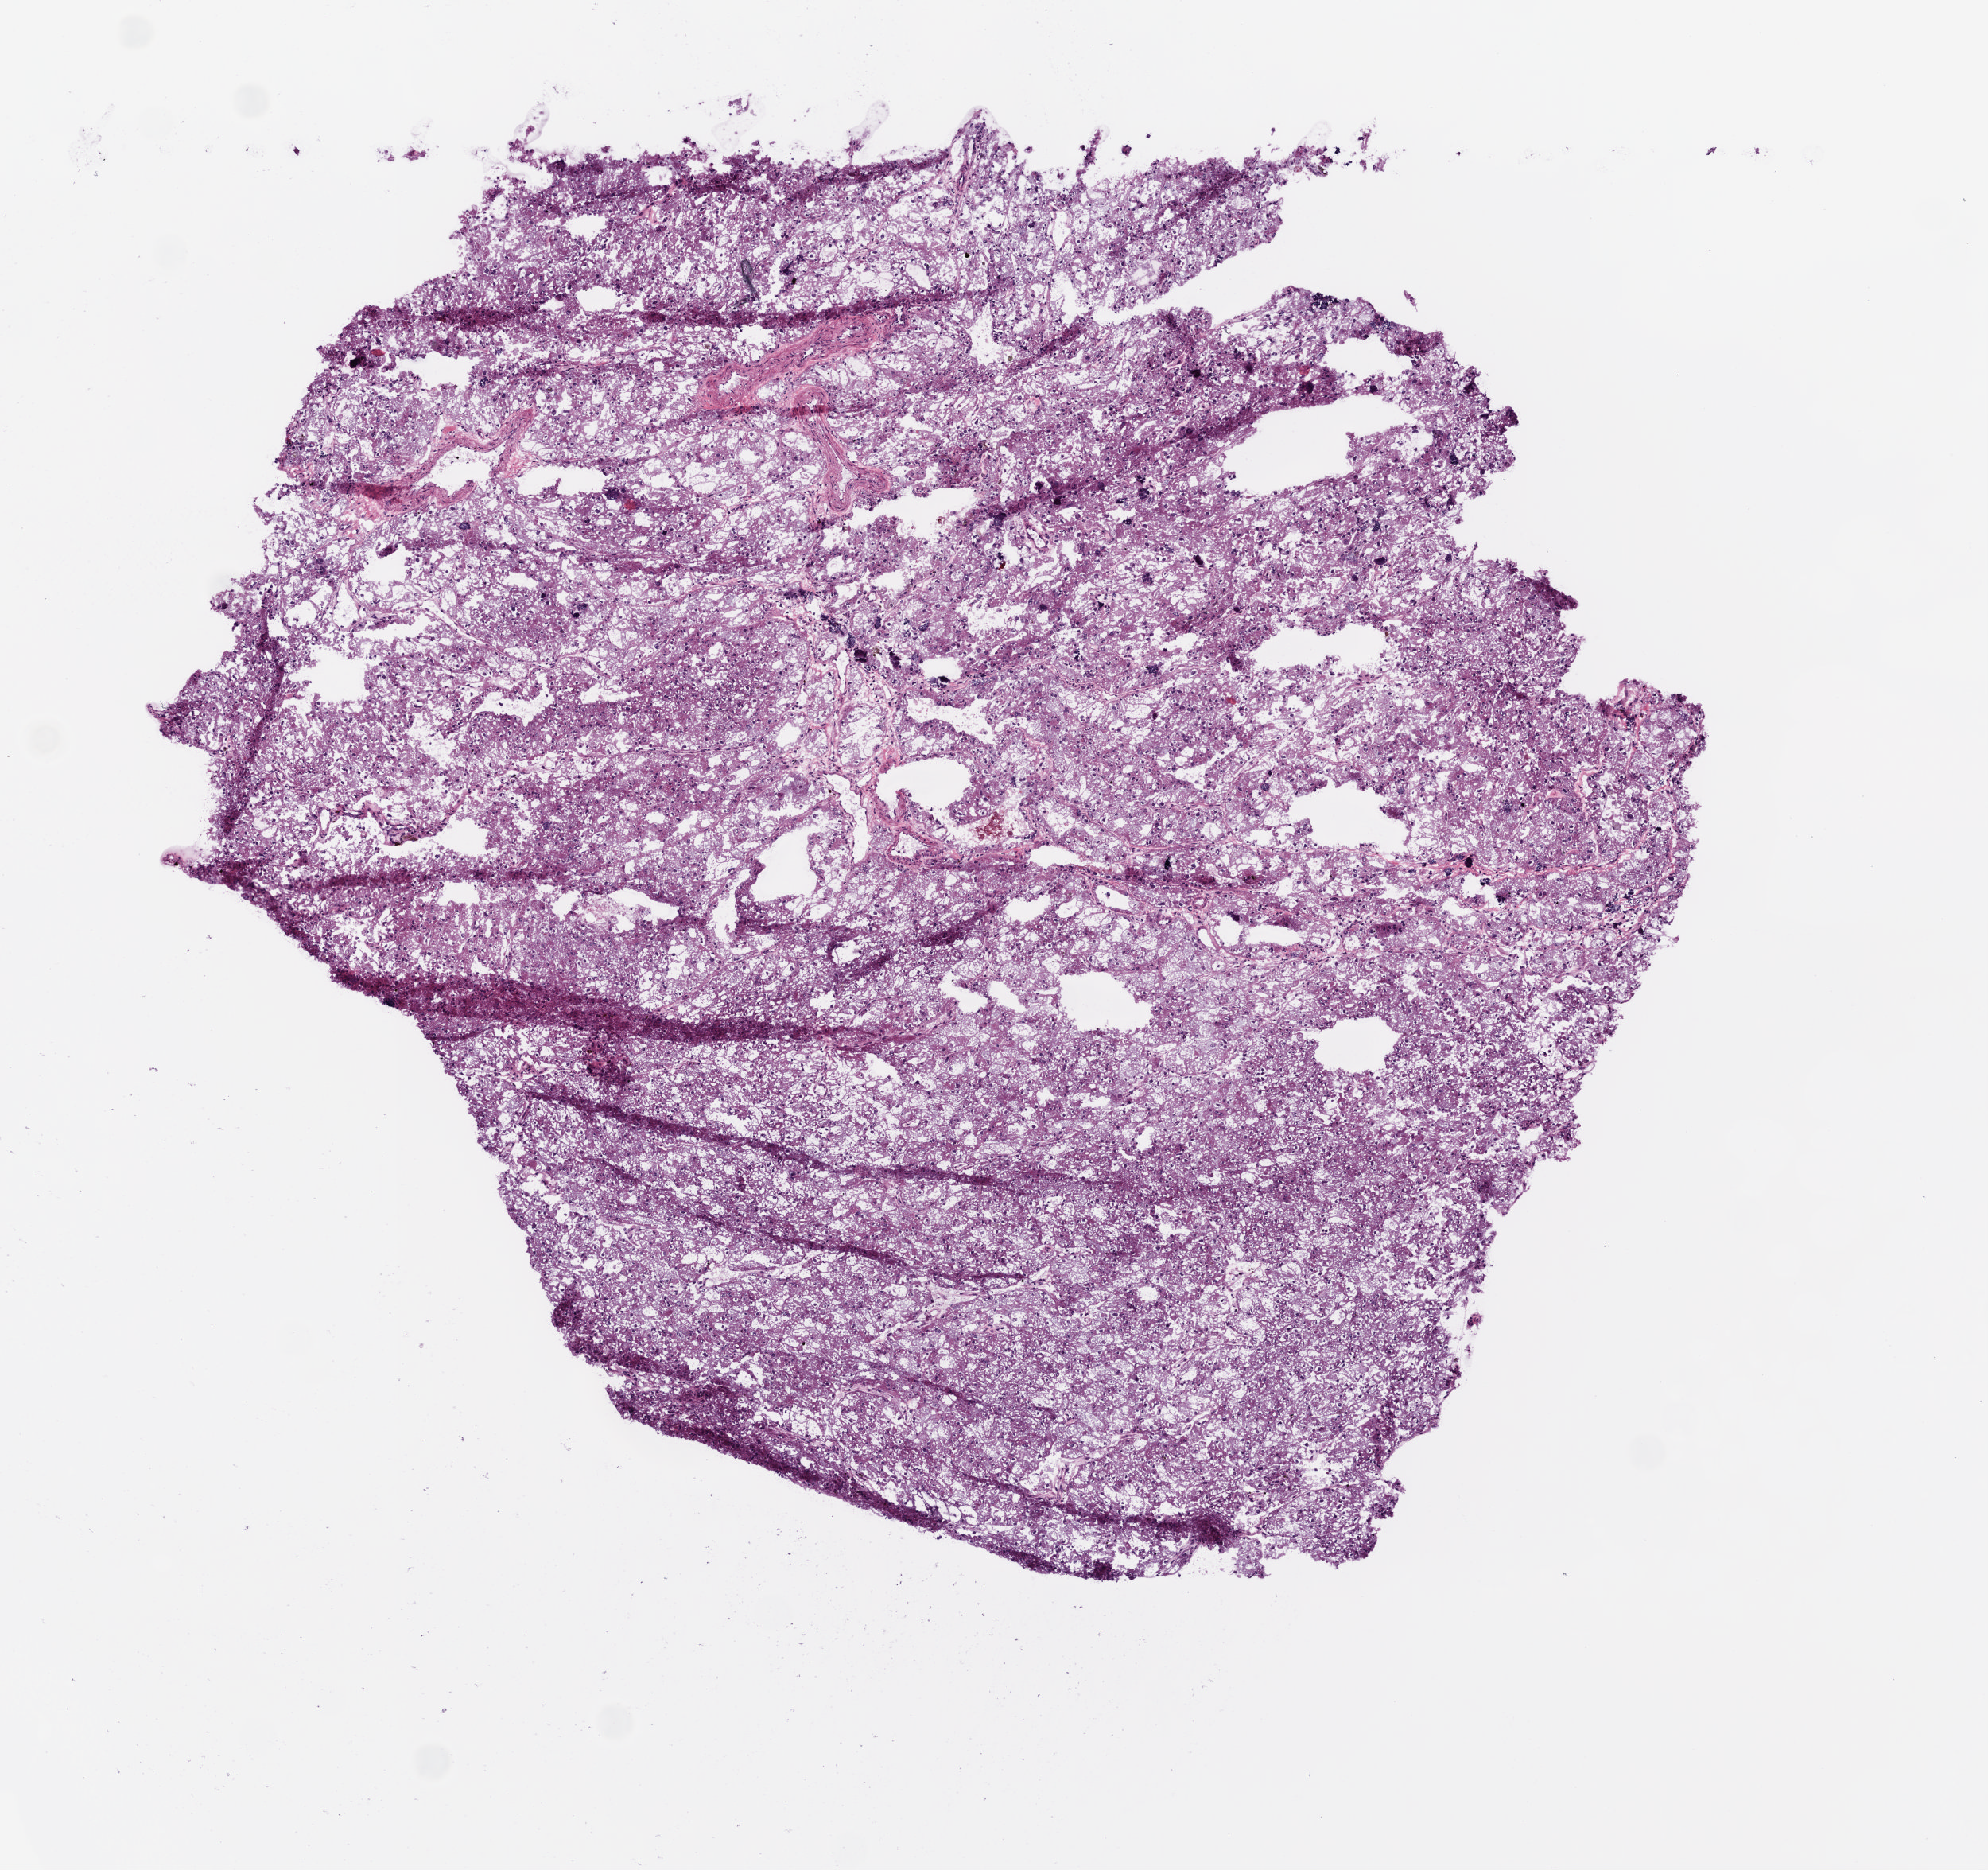
H&E whole-slide image, a low-resolution overview of the entire scanned area, about 5.0 x 4.7 mm (from a 20x scan); frozen section from the top of the tissue portion; sample: primary tumour, kidney. Male patient; age at initial diagnosis 63 years. Pathologist review of this section (percent, as recorded): tumour cells 90%, tumour nuclei 80%, normal cells 0%, stromal cells 10%, necrosis 0%.
* AJCC pathologic stage: I
* pathologic diagnosis: Clear cell adenocarcinoma, NOS
* laterality: left